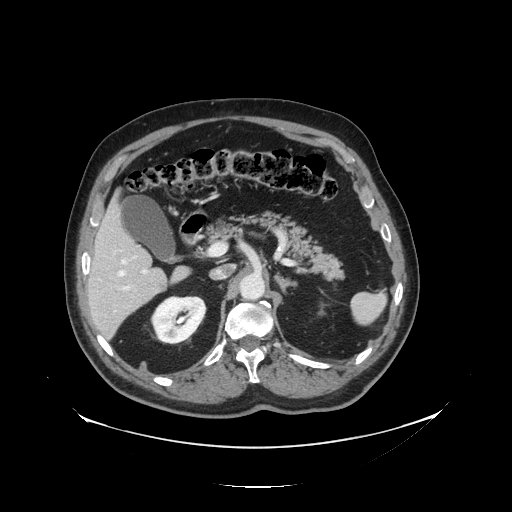
Contrast-enhanced abdominal CT, one axial slice; slice 75 of 138 in the series (ordered by position); intravenous contrast given; soft-tissue window (W 400 / L 40 HU); 2.5 mm slice thickness; 512 × 512 image matrix, field of view 497 × 497 mm. Male patient, age 77 years. From the clinical record (not read from this slice): diagnosis: colorectal cancer liver metastases, imaged before liver resection; multiple liver metastases: no.
Outlined on this slice (manually delineated by an expert):
- hepatic veins: bounding box (x1, y1, x2, y2) in pixels: (118, 260, 126, 276)
- liver: (86, 202, 175, 339)
- planned liver remnant (the part of the liver to remain after resection): (87, 202, 154, 287)
- portal vein (with intrahepatic branches): (116, 269, 149, 312)
- liver metastasis: (160, 284, 166, 291)